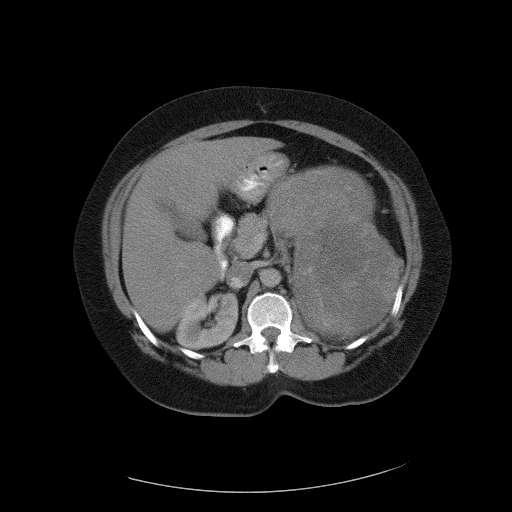
Contrast-enhanced abdominal CT, one axial slice; slice 65 of 90 in the series (ordered by position); reconstruction kernel FC01; 120 kVp; intravenous contrast given; soft-tissue window (W 400 / L 40 HU); 5 mm slice thickness; 512 × 512 image matrix, field of view 480 × 480 mm. Patient: female, 55 years. Case-level facts recorded for this patient, not image findings: diagnosis: adrenocortical carcinoma; tumour side: left adrenal; tumour size at pathology: 22 cm; Ki-67 index: 10 %; stage (as recorded): 3.
Structures marked on this image (semi-automatically segmented with operator editing):
- mass: box from (x=269, y=166) to (x=399, y=335) px